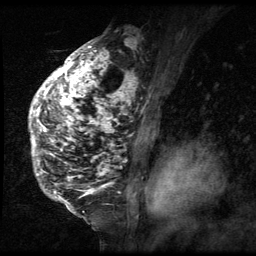
Breast MRI (dynamic contrast-enhanced), one sagittal slice; position 40 of 64 along the scan axis; 3 images stored at this slice position (order not interpretable as contrast timing); 1.5 T; TE 4.2 ms, TR 9 ms; 256 × 256 image matrix, field of view 180 × 180 mm. Female patient, age 50 years. Case-level facts recorded for this patient, not image findings: setting: breast cancer imaged before/during neoadjuvant chemotherapy; receptor status: triple-negative.
Structures marked on this image (semi-automatic segmentation, software-assisted and operator-edited):
- analysis volume of interest (the breast-tissue region the enhancement analysis was run in; not a lesion): bounding box (x1, y1, x2, y2) in pixels: (28, 39, 140, 212)
- tumour enhancement mask (voxels above the 140 % enhancement threshold inside the analysis volume of interest): (29, 39, 140, 212)